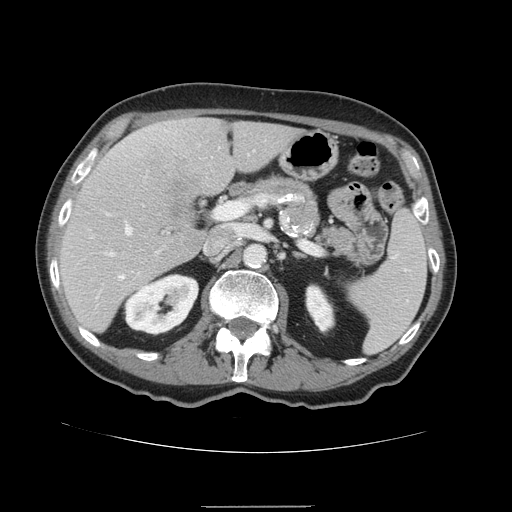
Contrast-enhanced abdominal CT, one axial slice. Position 85 of 168 along the scan axis. 120 kVp. Soft-tissue window (W 400 / L 40 HU). 512 × 512 image matrix, field of view 386 × 386 mm. Male patient, age 74 years. Case-level facts recorded for this patient, not image findings: diagnosis: colorectal cancer liver metastases, imaged before liver resection; multiple liver metastases: no; largest metastasis: 14.5 cm.
Structures marked on this image (outlined manually by an expert reader):
- hepatic veins: bounding box <121,224,132,278> (left, top, right, bottom; pixels)
- liver: <59,118,306,333>
- planned liver remnant (the part of the liver to remain after resection): <59,122,305,333>
- portal vein (with intrahepatic branches): <104,203,240,260>
- liver metastasis: <165,170,200,218>